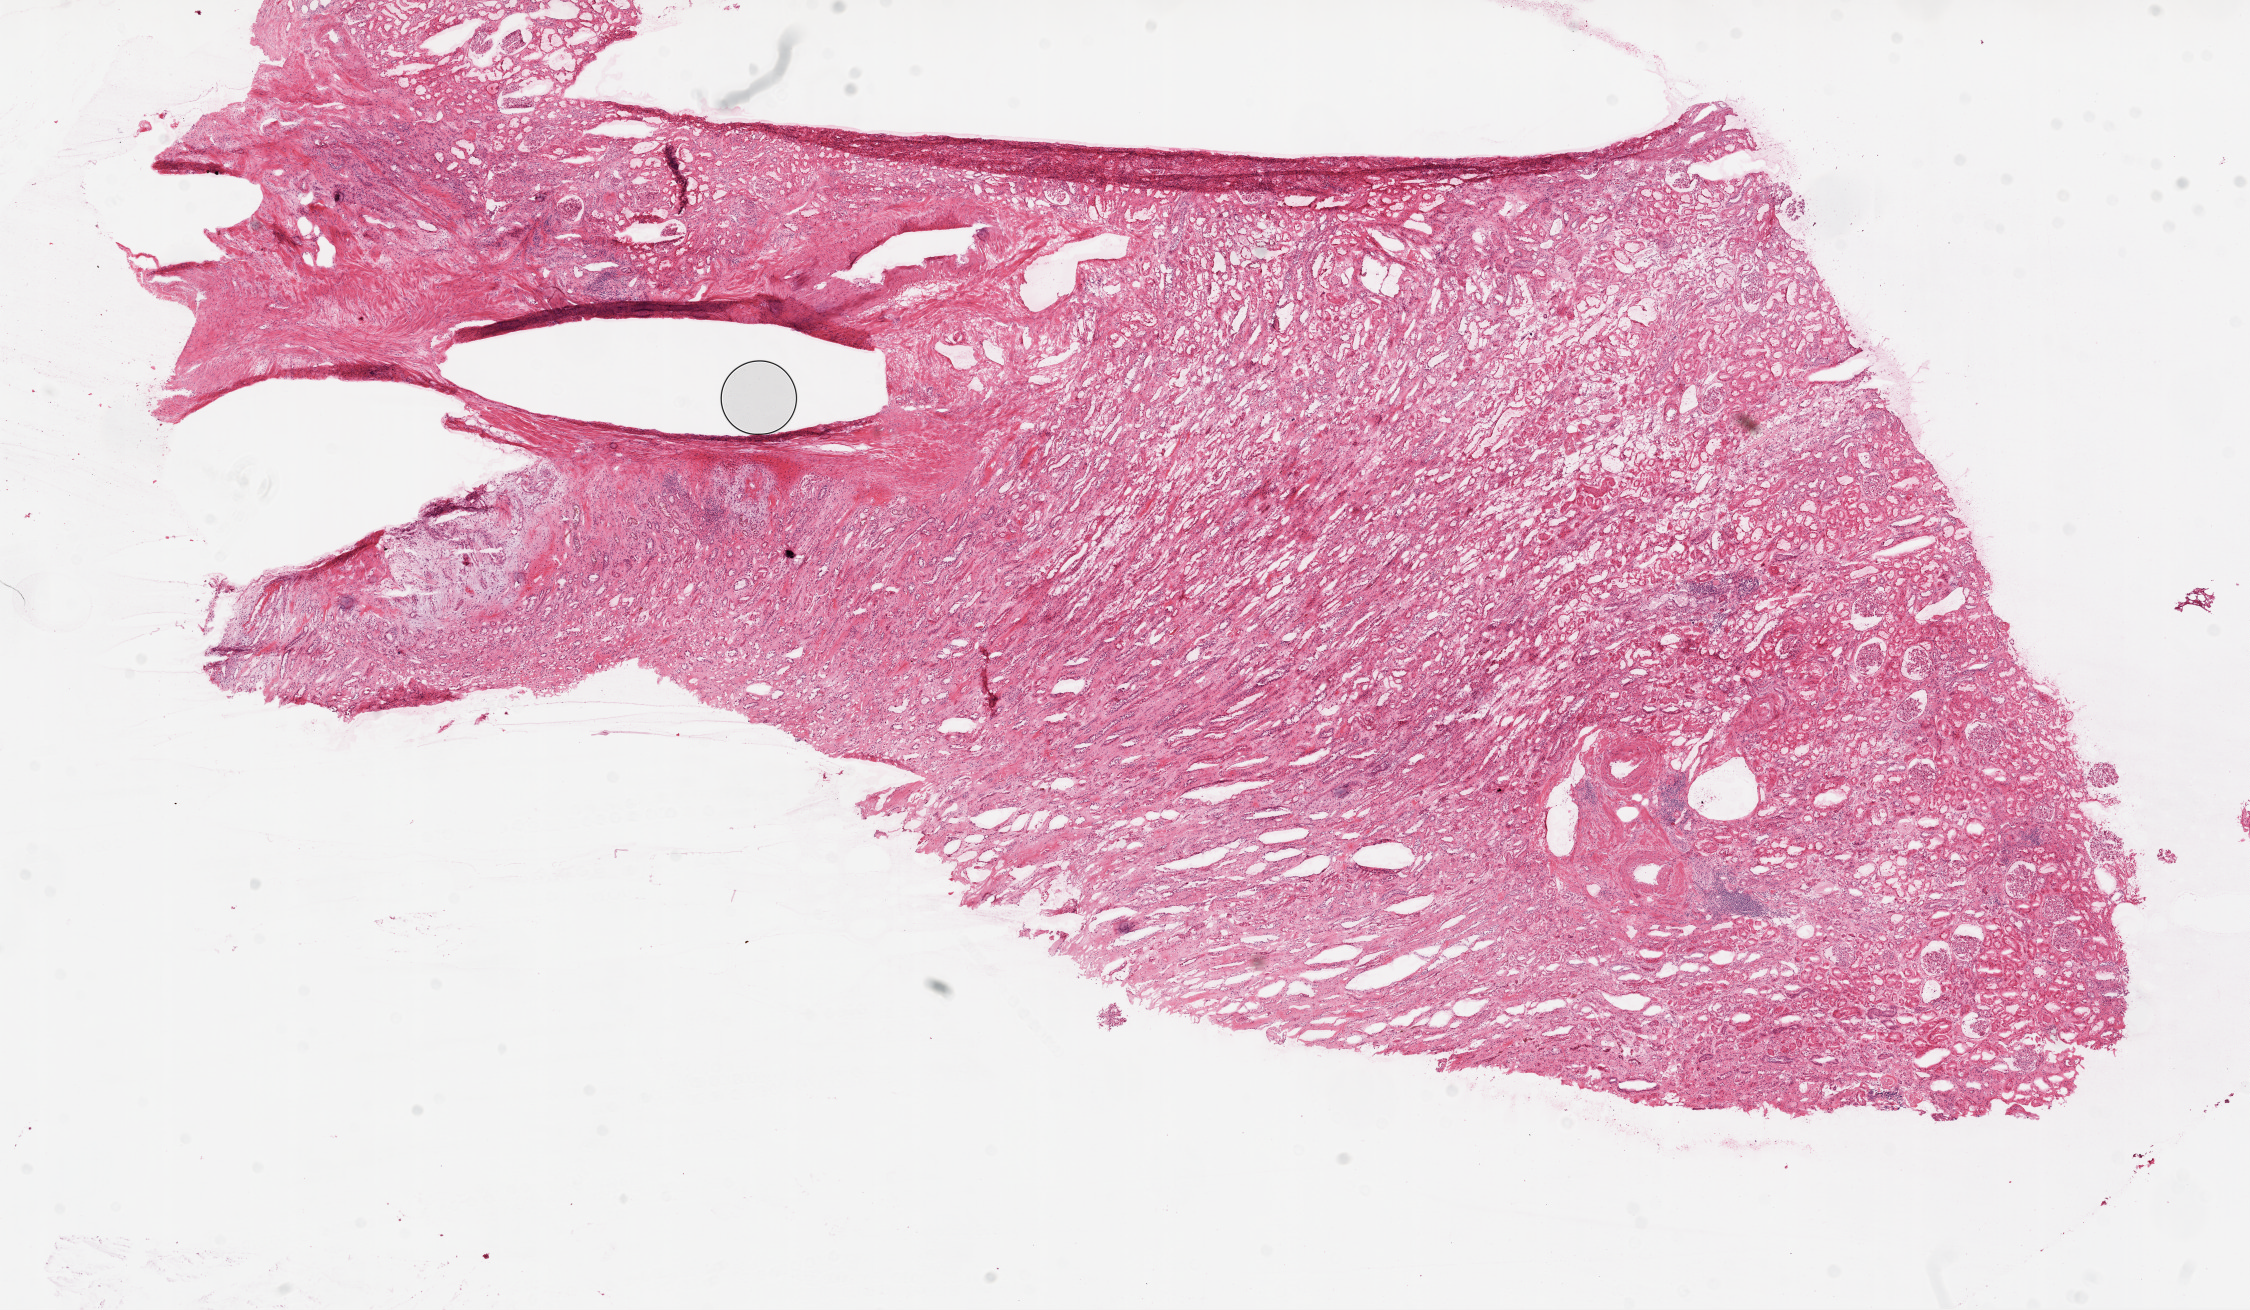
Whole-slide histology image, Hematoxylin and eosin (H&E) stained, whole scanned area (about 18.1 x 10.5 mm) shown as a low-resolution overview. Frozen section from the top of the tissue portion. Solid tissue normal (non-tumour tissue) sample from the kidney. Male, age 65 years at initial diagnosis.
This section: solid tissue normal (non-tumour) sample from the same patient. Patient diagnosis: Clear cell adenocarcinoma, NOS.